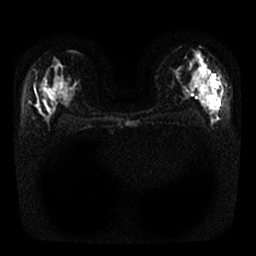
Breast MRI, one axial slice. Slice 15 of 25 in the series (ordered by position). Diffusion-weighted series; image 2 of 4 stored at this slice position (different b-values; order by instance number). 1.5 T. 4 mm slice thickness. 256 × 256 image matrix. Female patient.
Annotated regions visible in this slice (outlined manually by an expert reader):
- tumour on diffusion-weighted imaging: bounding box <204,69,213,83> (left, top, right, bottom; pixels)